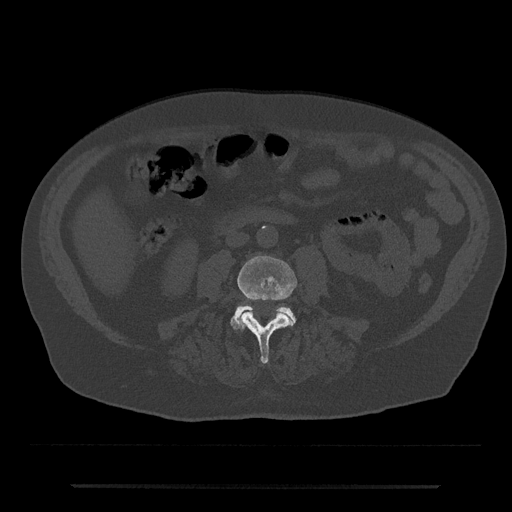
CT including the spine, one axial slice; slice 390 of 797 in the series (ordered by position); 120 kVp; bone window (W 1800 / L 400 HU); 512 × 512 image matrix. Patient: male, 80 years. Case-level facts recorded for this patient, not image findings: primary cancer: prostate; vertebrae with lytic lesions (as recorded): L1, T11.
Outlined on this slice (semi-automatically segmented with operator editing):
- L3 vertebra: bounding box [x1, y1, x2, y2] px = [237, 256, 298, 363]
- L4 vertebra: [230, 305, 296, 329]